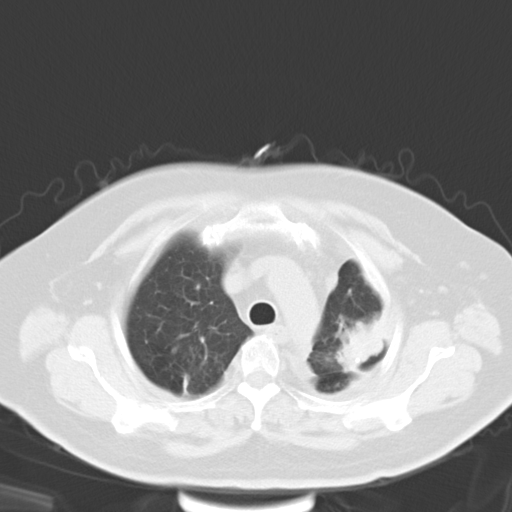
Chest CT, one axial slice; slice 23 of 29 in the series (ordered by position); lung window (W 1500 / L -600 HU); 8 mm slice thickness; 512 × 512 image matrix. Female patient, age 69 years. From the clinical record (not read from this slice): clinical TNM (as recorded): T3 N0 M0.
Outlined on this slice (rectangle marked by the reading radiologist):
- lung tumour (recorded histology: adenocarcinoma): bounding box <341,306,386,374> (left, top, right, bottom; pixels)